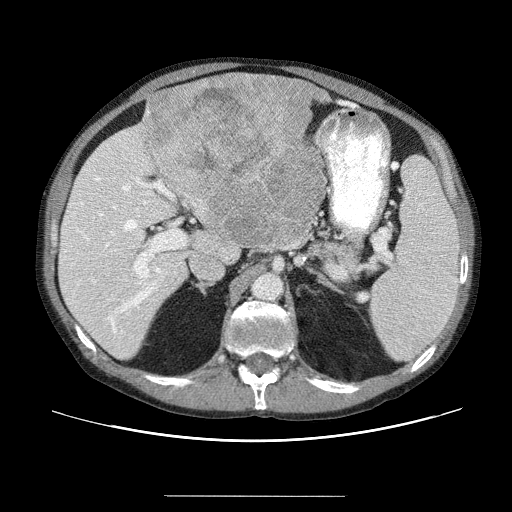
Contrast-enhanced abdominal CT (liver protocol), one axial slice; slice 27 of 69 in the series (ordered by position); reconstruction kernel STANDARD; 120 kVp; soft-tissue window (W 400 / L 40 HU); 2.5 mm slice thickness; 512 × 512 image matrix, field of view 380 × 380 mm. Case-level facts recorded for this patient, not image findings: diagnosis: hepatocellular carcinoma (patient treated with transarterial chemoembolisation; whether this scan precedes or follows treatment is not stated here); TNM stage (as recorded): Stage-IVB; Child-Pugh class: B; tumour differentiation: poorly differentiated.
Annotated regions visible in this slice (semi-automatically segmented with operator editing):
- liver parenchyma outside the tumour (the mass and vessels are separate outlines, so this box may not span the whole liver): bounding box (x1, y1, x2, y2) in pixels: (58, 101, 326, 358)
- mass: (135, 75, 328, 254)
- liver vessels: (63, 154, 222, 342)